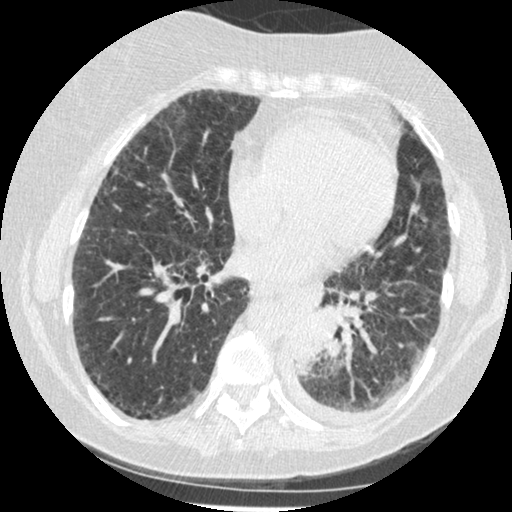
Axial slice from a low-dose chest CT screening exam. Third screening round (two years after baseline). Lung window (W 1500 / L -600 HU). 1.25 mm slice thickness. Slice 254 of 341 in the series. Female, age 60 years at enrolment. Former smoker at enrolment.
Lesion marked by an expert reader, bounding box <278,302,343,377> (left, top, right, bottom; pixels). Reader record for this screening exam (exam-level; its link to the box is not recorded): non-calcified nodule or mass ≥4 mm, left lower lobe, 54 × 38 mm, smooth margins, soft tissue attenuation, pre-existing on the prior screen: yes; interval growth: yes. Official screen result: positive, other.